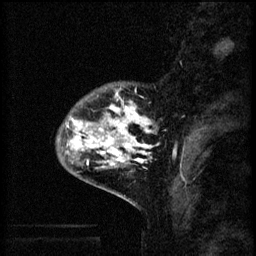
Breast MRI (dynamic contrast-enhanced), one sagittal slice; position 14 of 60 along the scan axis; 3 images stored at this slice position (order not interpretable as contrast timing); 1.5 T; TE 4.2 ms, TR 8.2 ms; 2 mm slice thickness; 256 × 256 image matrix. Patient: female, 41 years.
Annotated regions visible in this slice (semi-automatically segmented with operator editing):
- analysis volume of interest (the breast-tissue region the enhancement analysis was run in; not a lesion): bounding box (x1, y1, x2, y2) in pixels: (57, 84, 158, 175)
- tumour enhancement mask (voxels above the 70 % enhancement threshold inside the analysis volume of interest): (66, 94, 158, 169)